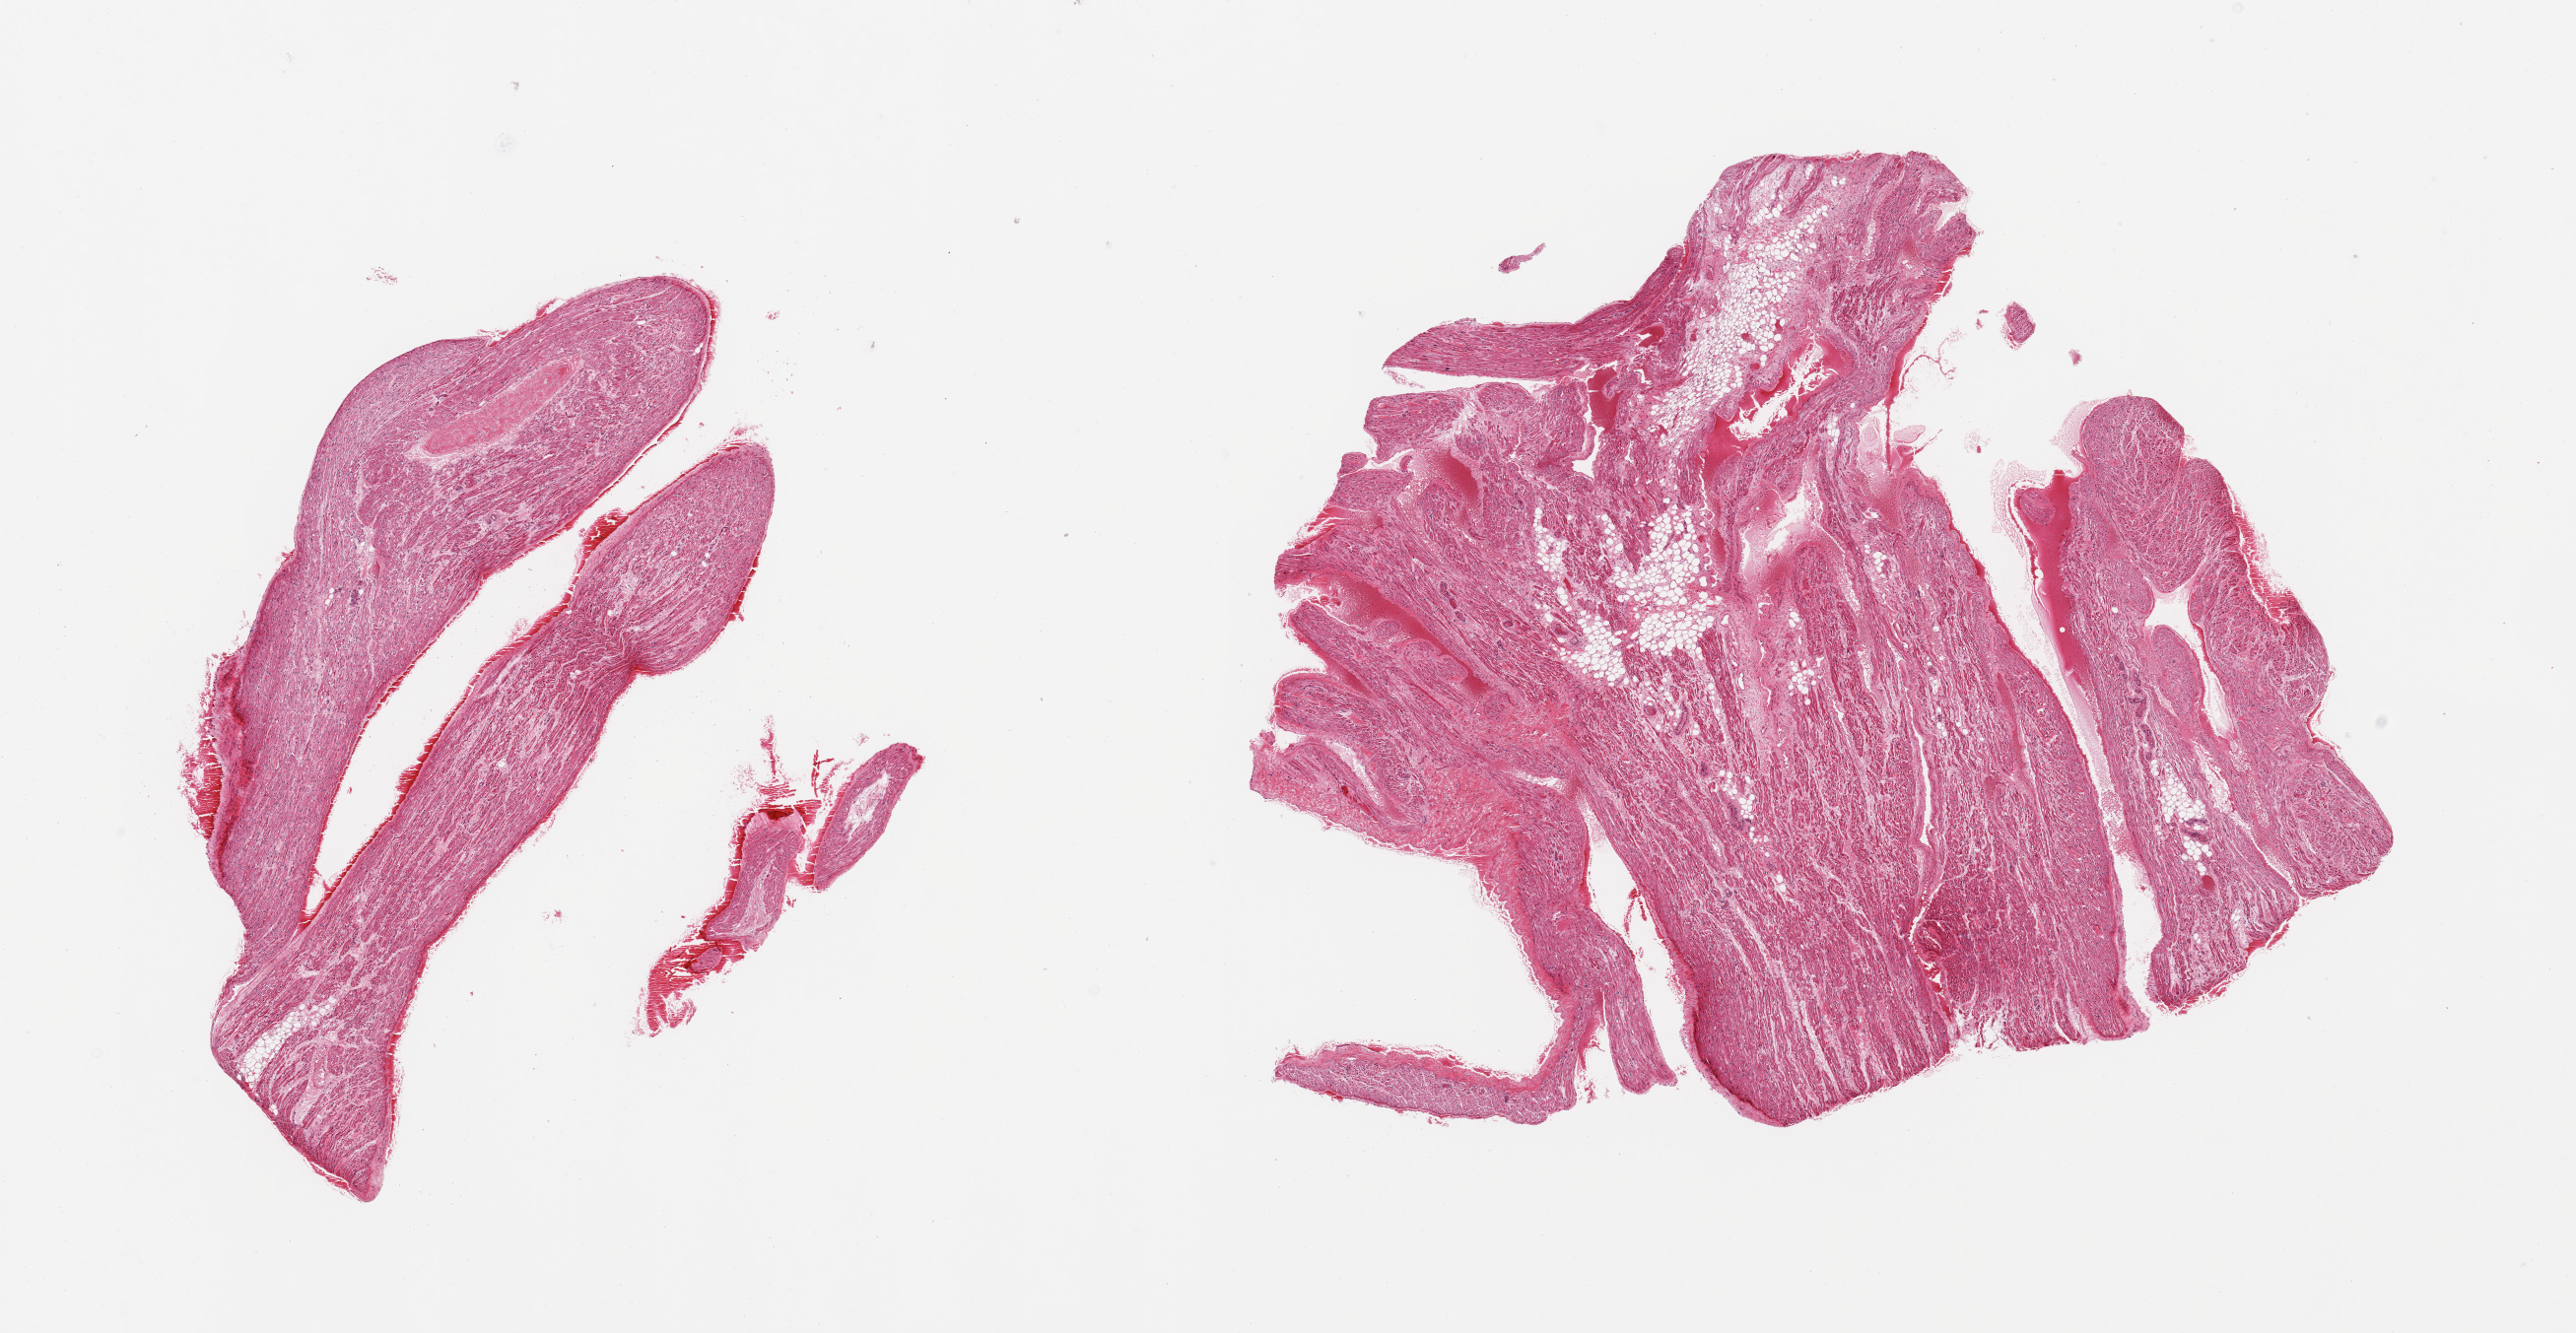
Hematoxylin and eosin (H&E) whole-slide image — a low-resolution overview of the entire scanned area, about 20.7 x 10.7 mm; PAXgene-fixed paraffin-embedded (PFPE) section; target tissue: auricular appendage; donor tissue sample.
Review note (as recorded): 2 pieces; larger piece with 10% internal fat; no obvious inflammatory lesion.